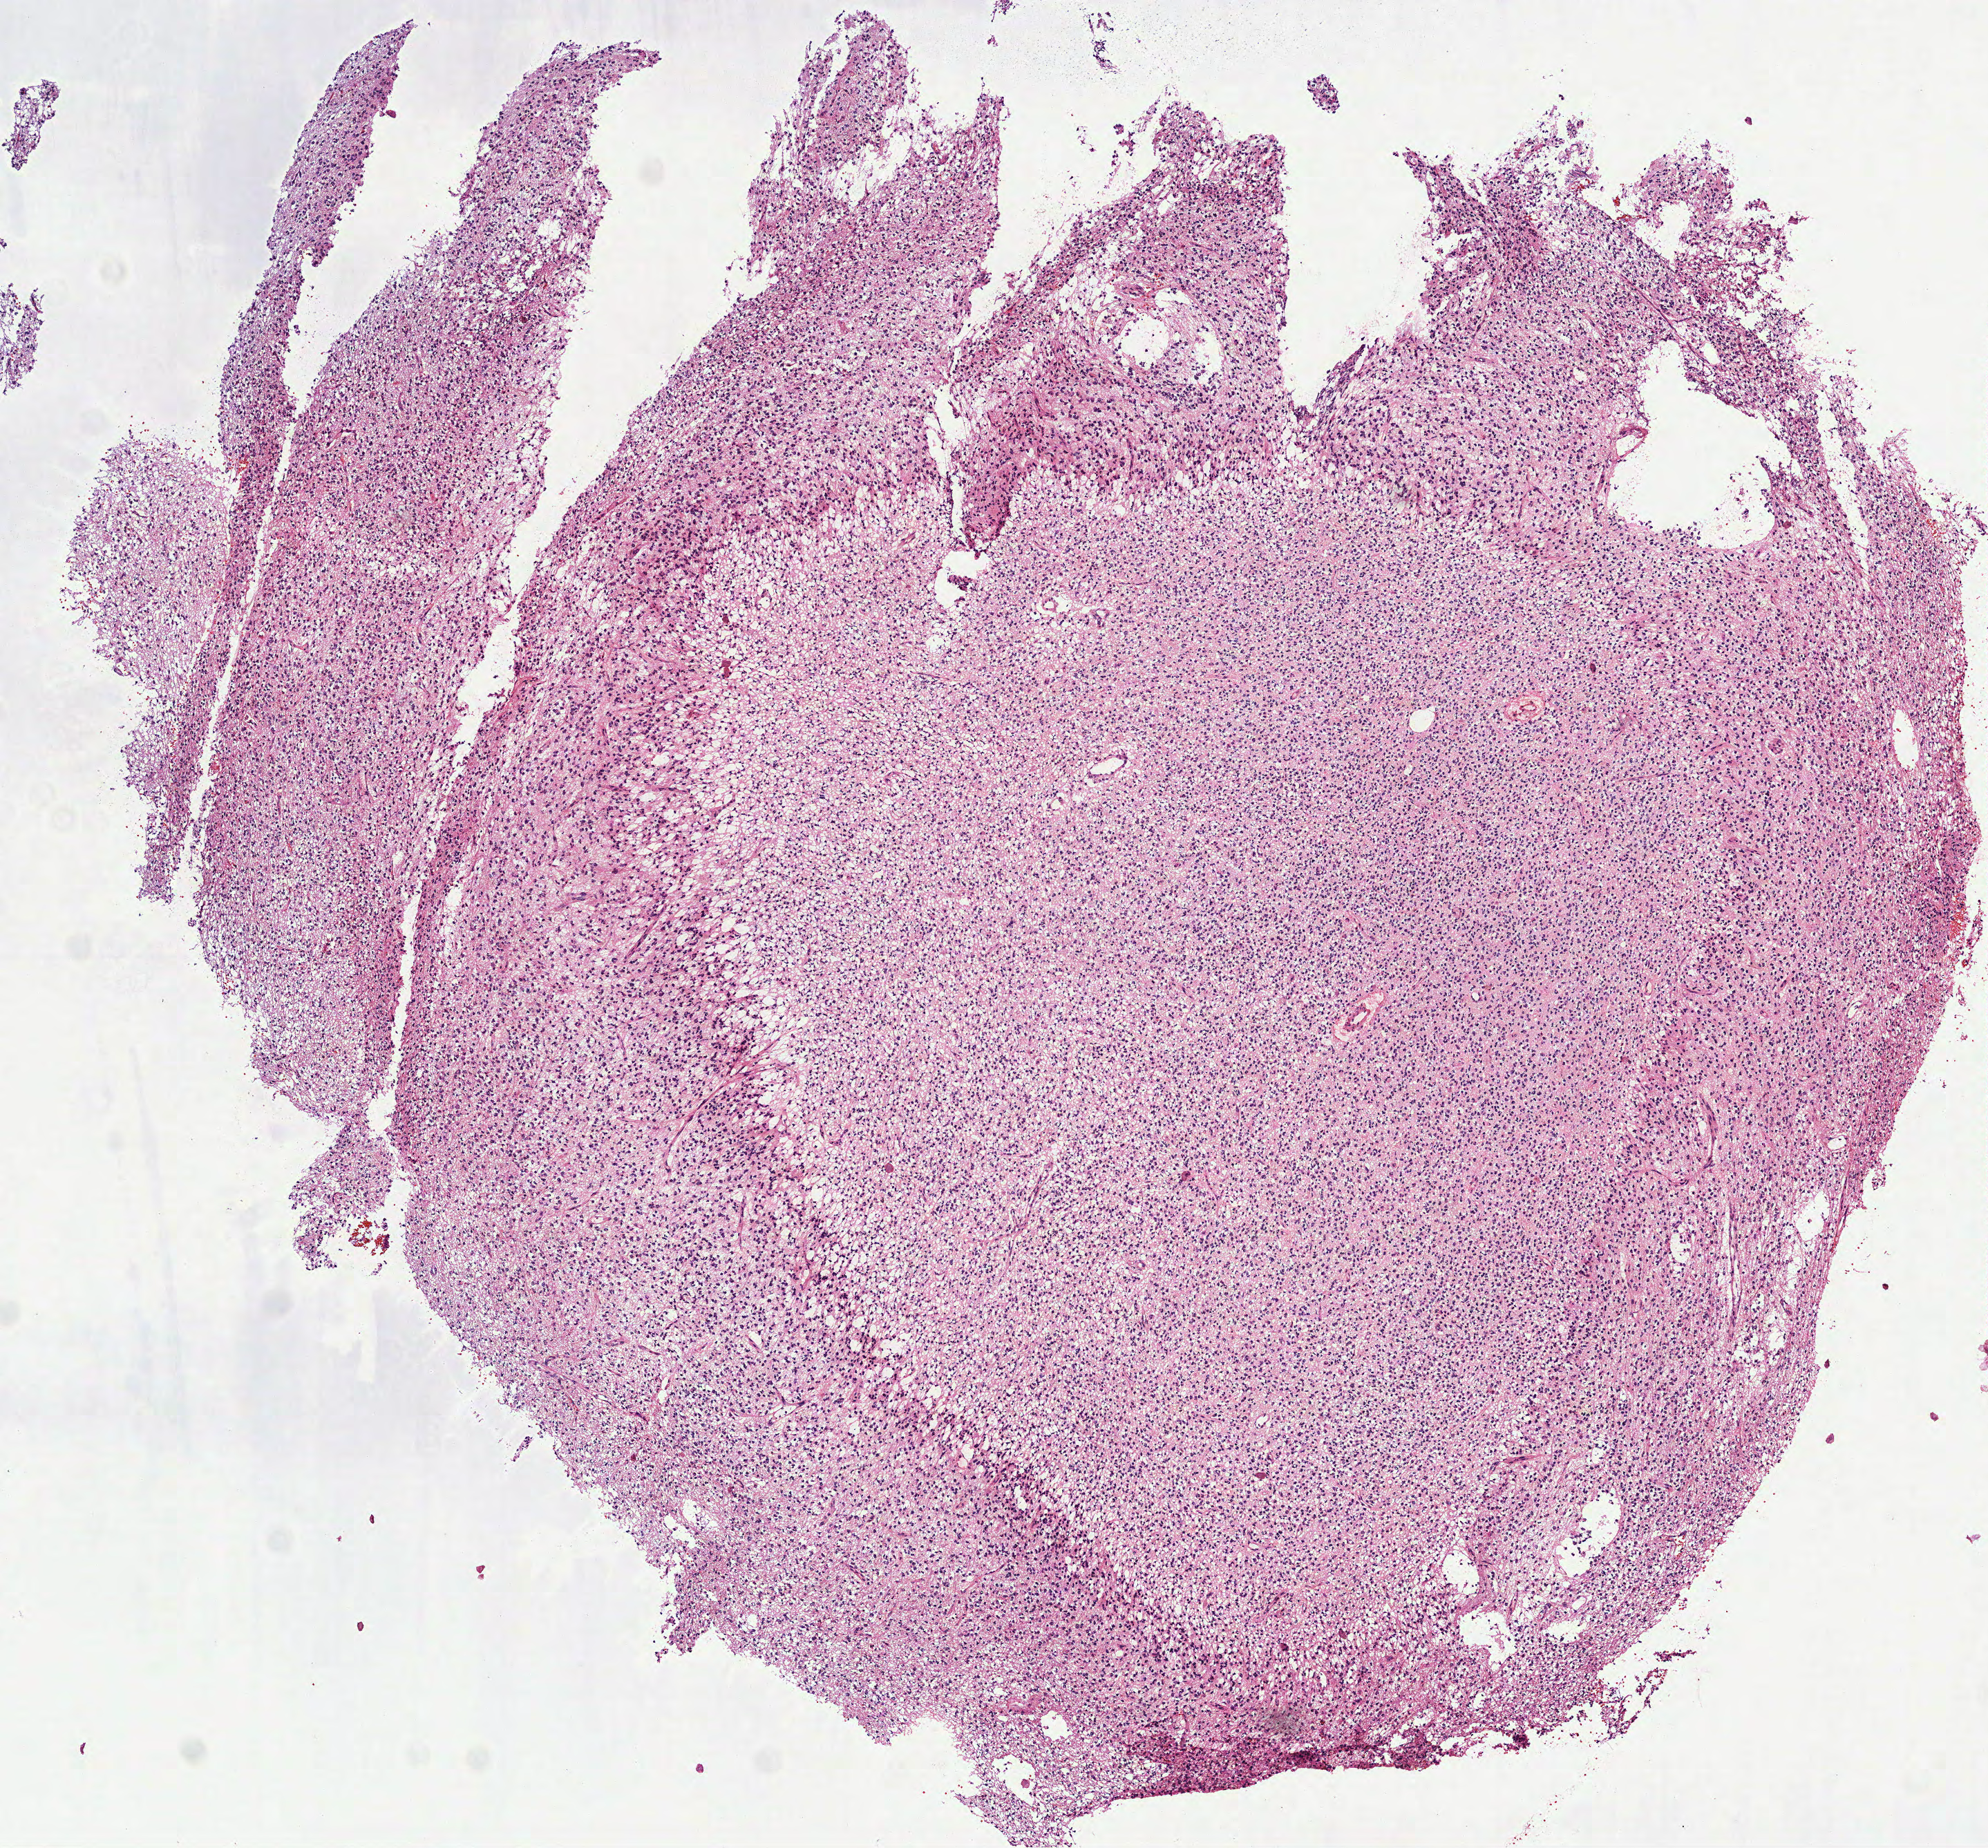
H&E-stained whole-slide image, low-resolution overview of the scanned area, about 5.8 x 5.4 mm (slide scanned at 40x). Frozen section. Sample: primary tumour, brain. Female patient; age at initial diagnosis 37 years. Histologic grade: G3 (poorly differentiated). Composition of this section per pathologist review: tumour cells 100%, tumour nuclei 85%, normal cells 0%, stromal cells 0%, necrosis 0%.
Pathologic diagnosis: Oligodendroglioma, anaplastic.